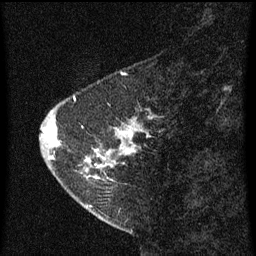
Breast MRI (dynamic contrast-enhanced), one sagittal slice; position 17 of 60 along the scan axis; dynamic contrast-enhanced series, image 2 of 3 at this slice position (ordered by acquisition); 1.5 T; TE 4.2 ms, TR 8 ms; 256 × 256 image matrix, field of view 180 × 180 mm. Patient: female, 47 years.
Structures marked on this image (semi-automatically segmented with operator editing):
- analysis volume of interest (the breast-tissue region the enhancement analysis was run in; not a lesion): bounding box (x1, y1, x2, y2) in pixels: (44, 94, 155, 199)
- tumour enhancement mask (voxels above the 70 % enhancement threshold inside the analysis volume of interest): (44, 98, 149, 169)